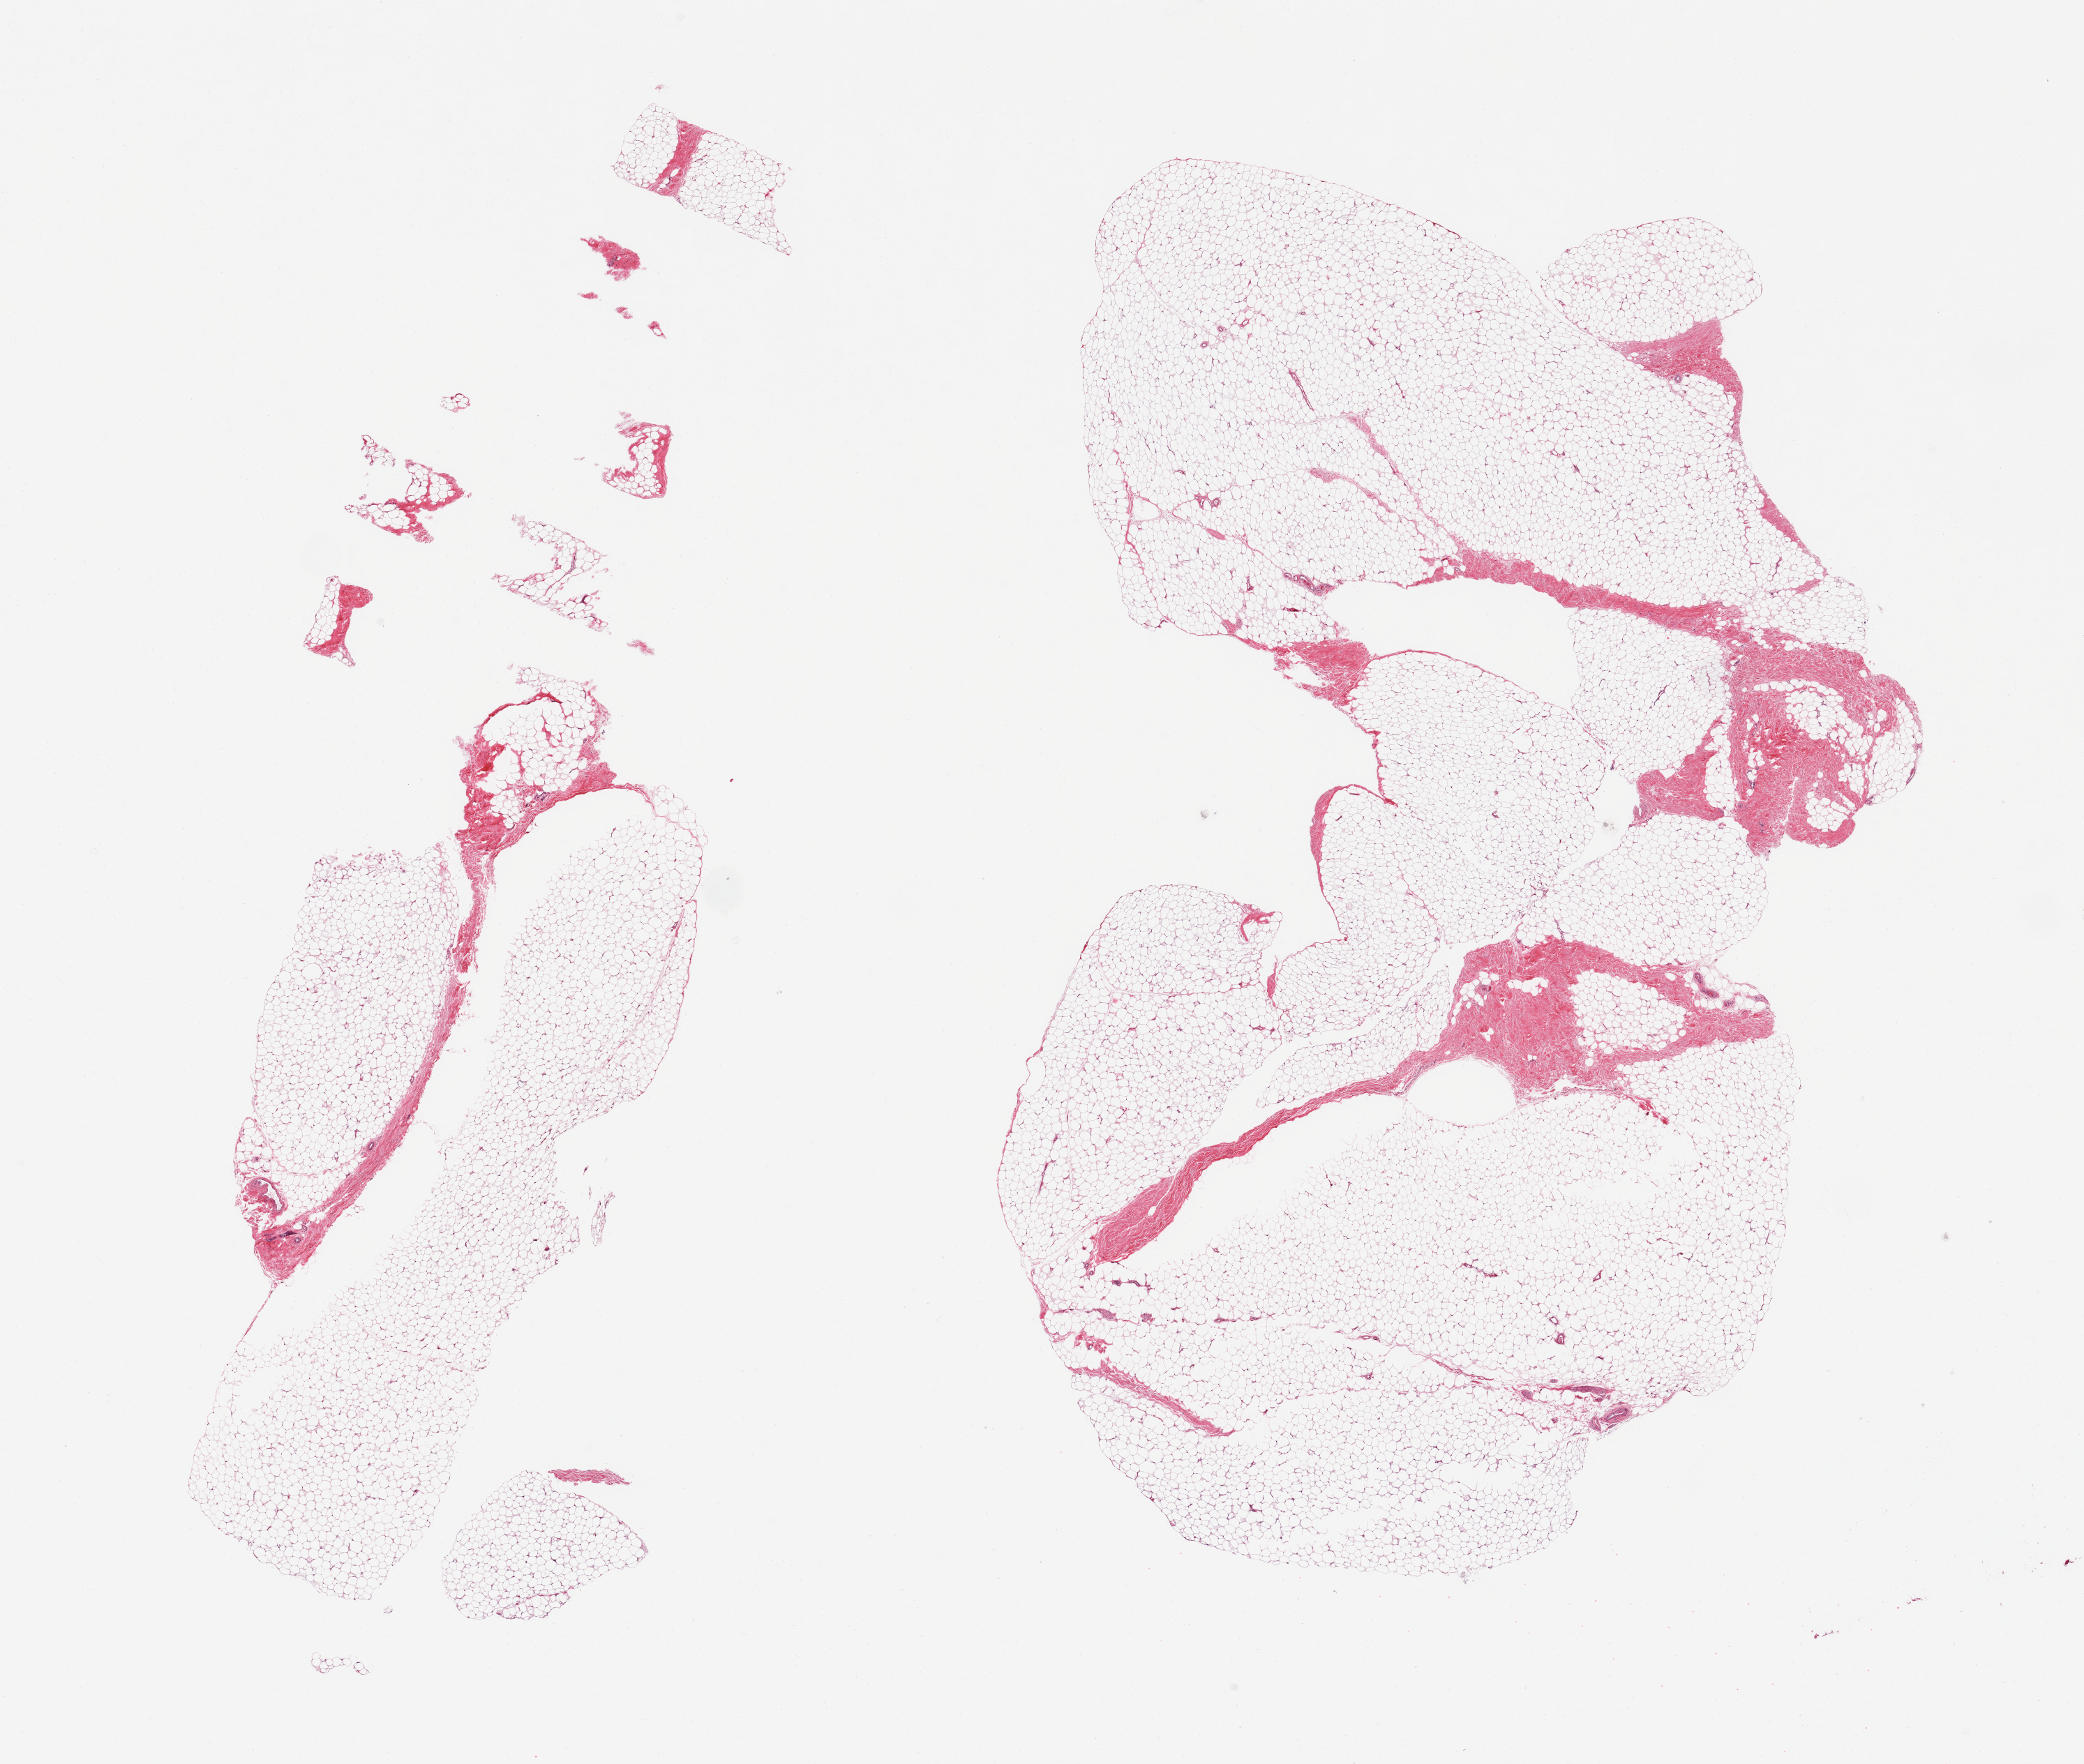
Hematoxylin and eosin (H&E) whole-slide image — shown as a low-resolution overview of the whole scanned area (about 23.6 x 20.0 mm, acquisition: 20x scan), PAXgene-fixed, paraffin-embedded tissue, section of breast (target tissue), tissue donor sample.
• pathologist's review note for this sample: 2 pieces, fibroadipose elements only